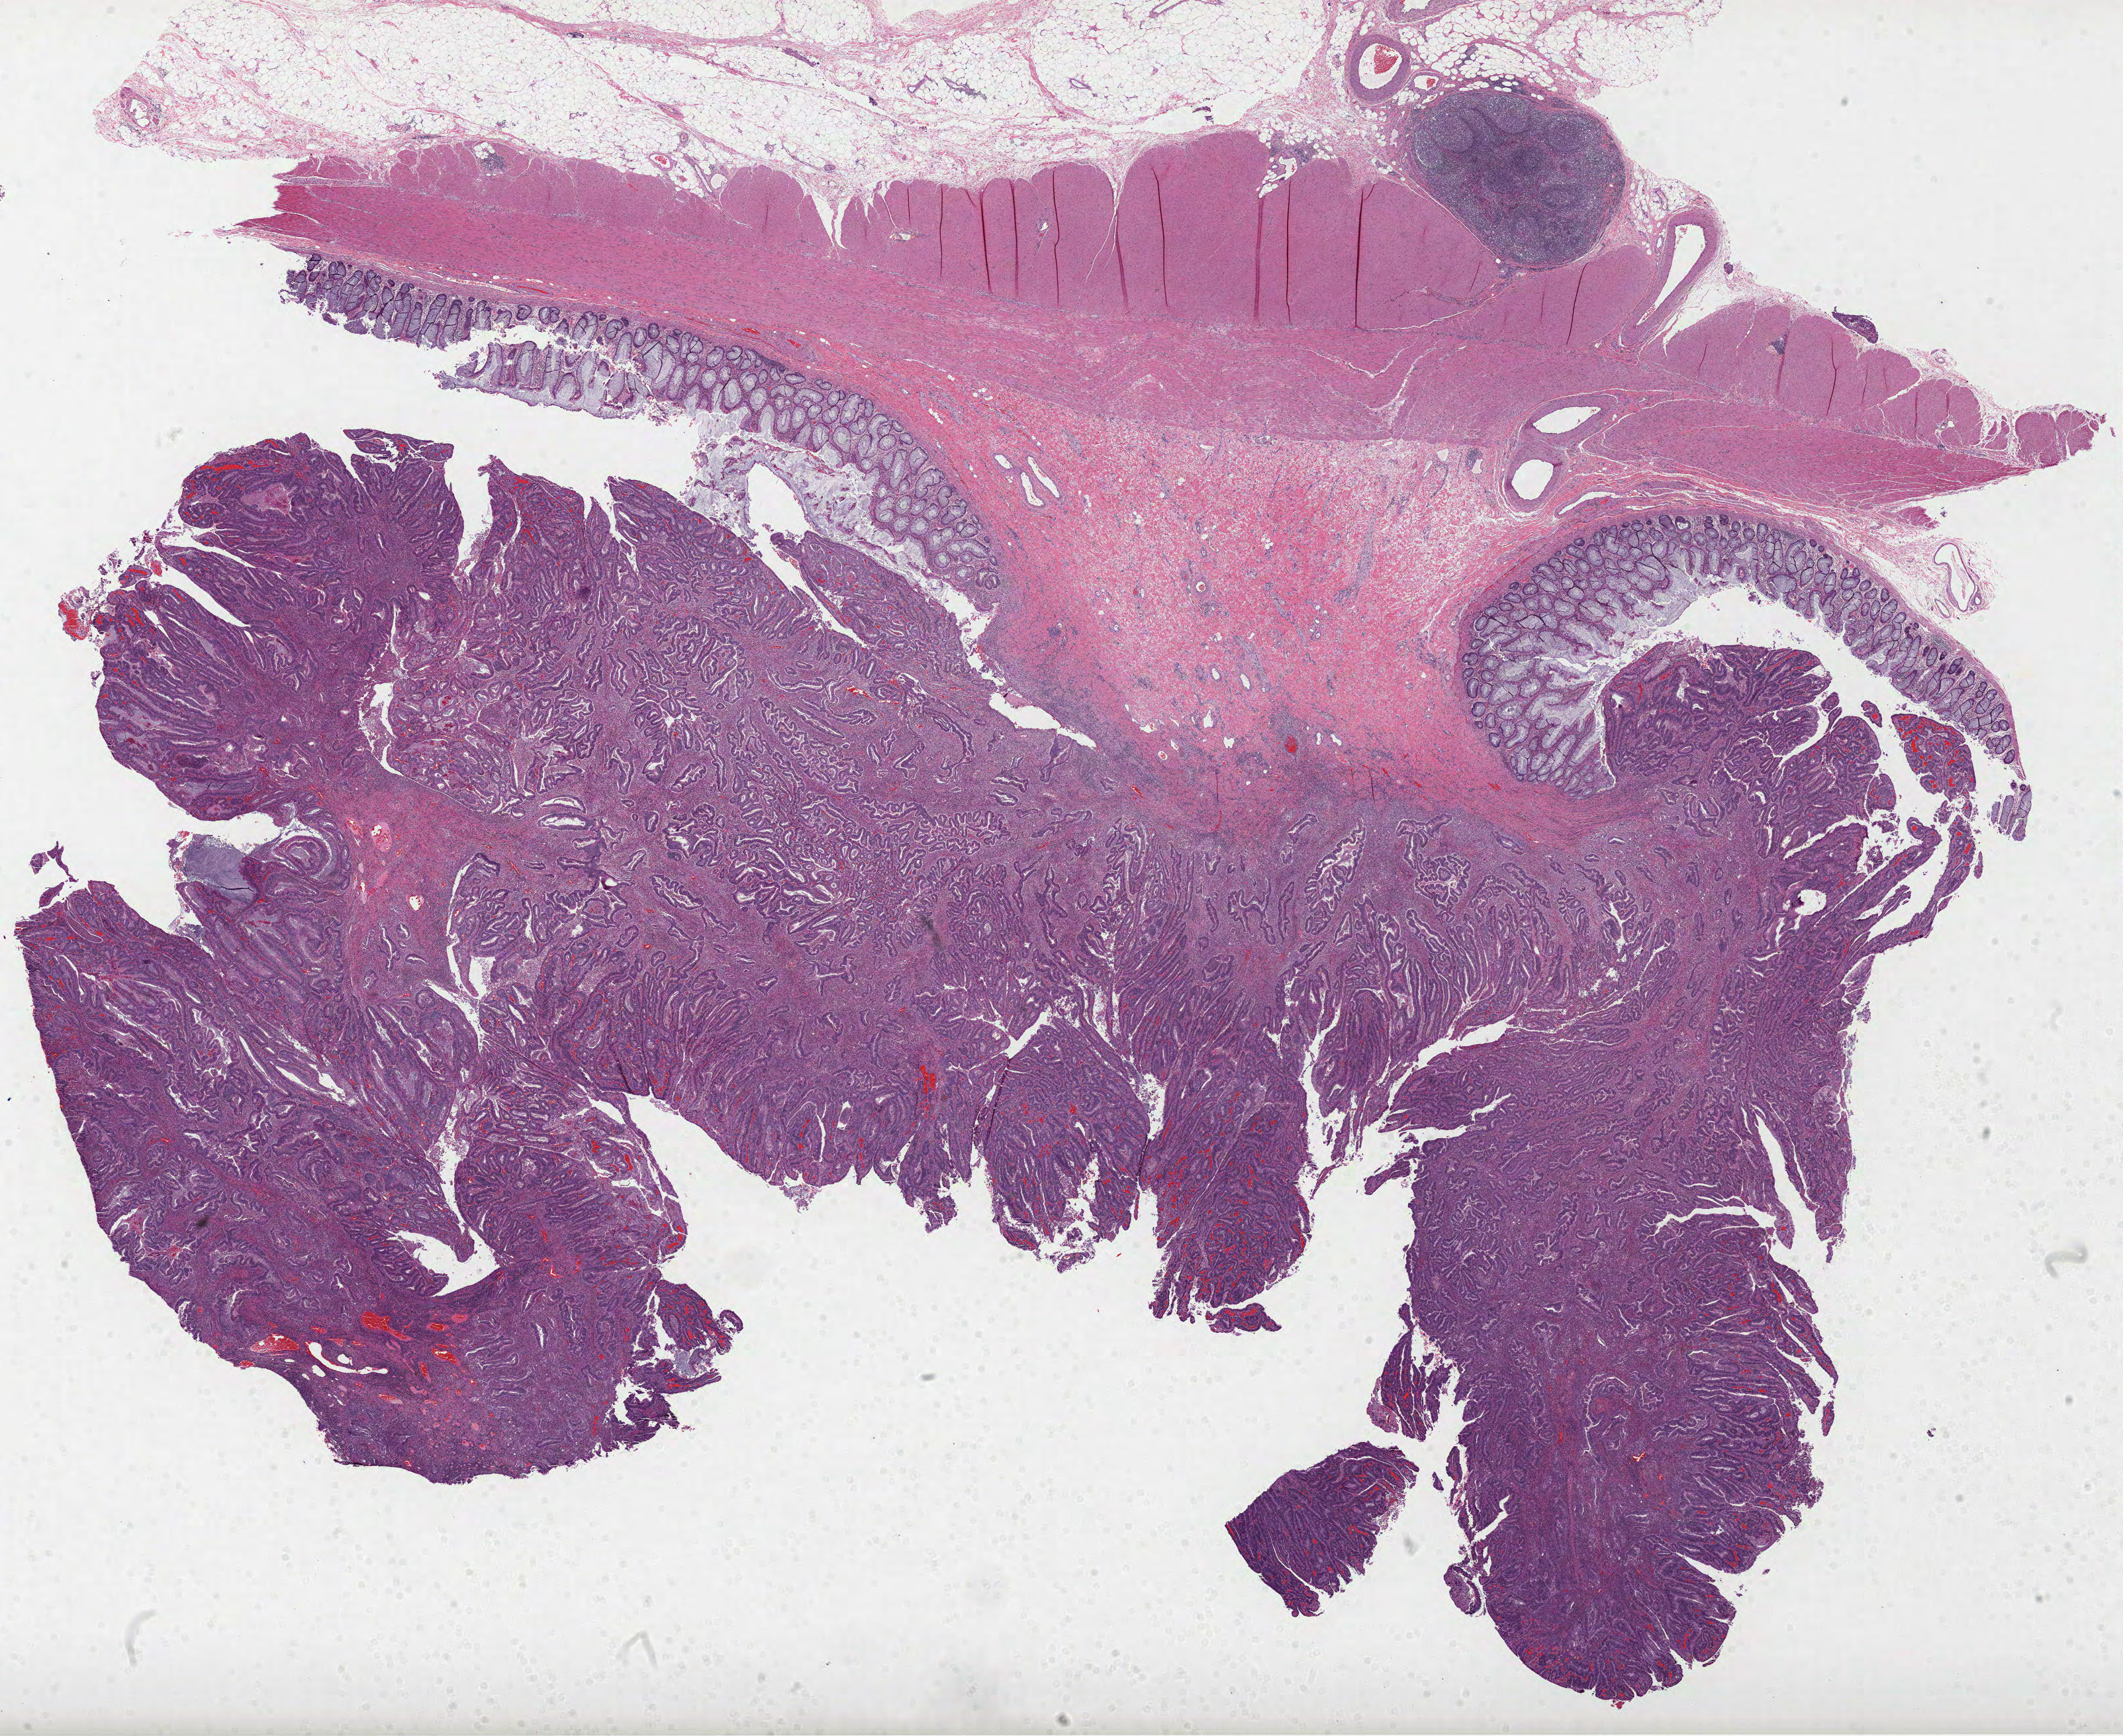
Digitized H&E tissue section (whole slide) — whole scanned area (about 25.9 x 21.1 mm, slide scanned at 40x) shown as a low-resolution overview; FFPE section; colon, primary tumour sample. Female patient; age at initial diagnosis 39 years.
AJCC pathologic stage: IIIB. Histologic diagnosis: Adenocarcinoma, NOS (sigmoid colon). Lymph nodes positive (case pathology): 3 of 108 examined.